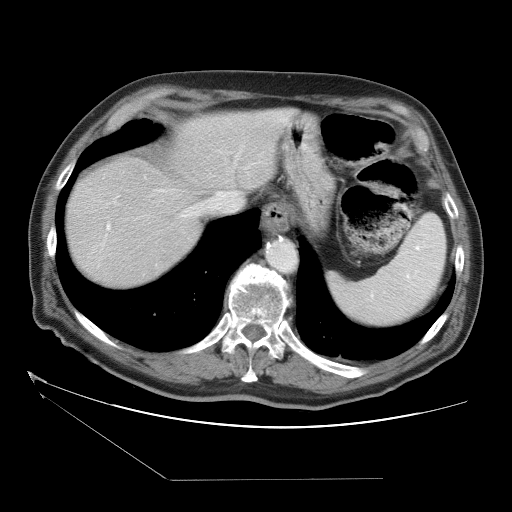
Contrast-enhanced abdominal CT (liver protocol), one axial slice; slice 29 of 38 in the series (ordered by position); reconstruction kernel STANDARD; 120 kVp; one of 2 acquisitions stored at this slice position; soft-tissue window (W 400 / L 40 HU); 5 mm slice thickness; 512 × 512 image matrix, field of view 400 × 400 mm. From the clinical record (not read from this slice): diagnosis: hepatocellular carcinoma (patient treated with transarterial chemoembolisation; whether this scan precedes or follows treatment is not stated here); TNM stage (as recorded): Stage-II; Child-Pugh class: A; tumour differentiation: moderately differentiated; tumour nodularity: multinodular.
Outlined on this slice (semi-automatically segmented with operator editing):
- abdominal aorta: bounding box (x1, y1, x2, y2) in pixels: (268, 243, 297, 272)
- liver parenchyma outside the tumour (the mass and vessels are separate outlines, so this box may not span the whole liver): (66, 108, 314, 286)
- liver vessels: (106, 197, 196, 231)